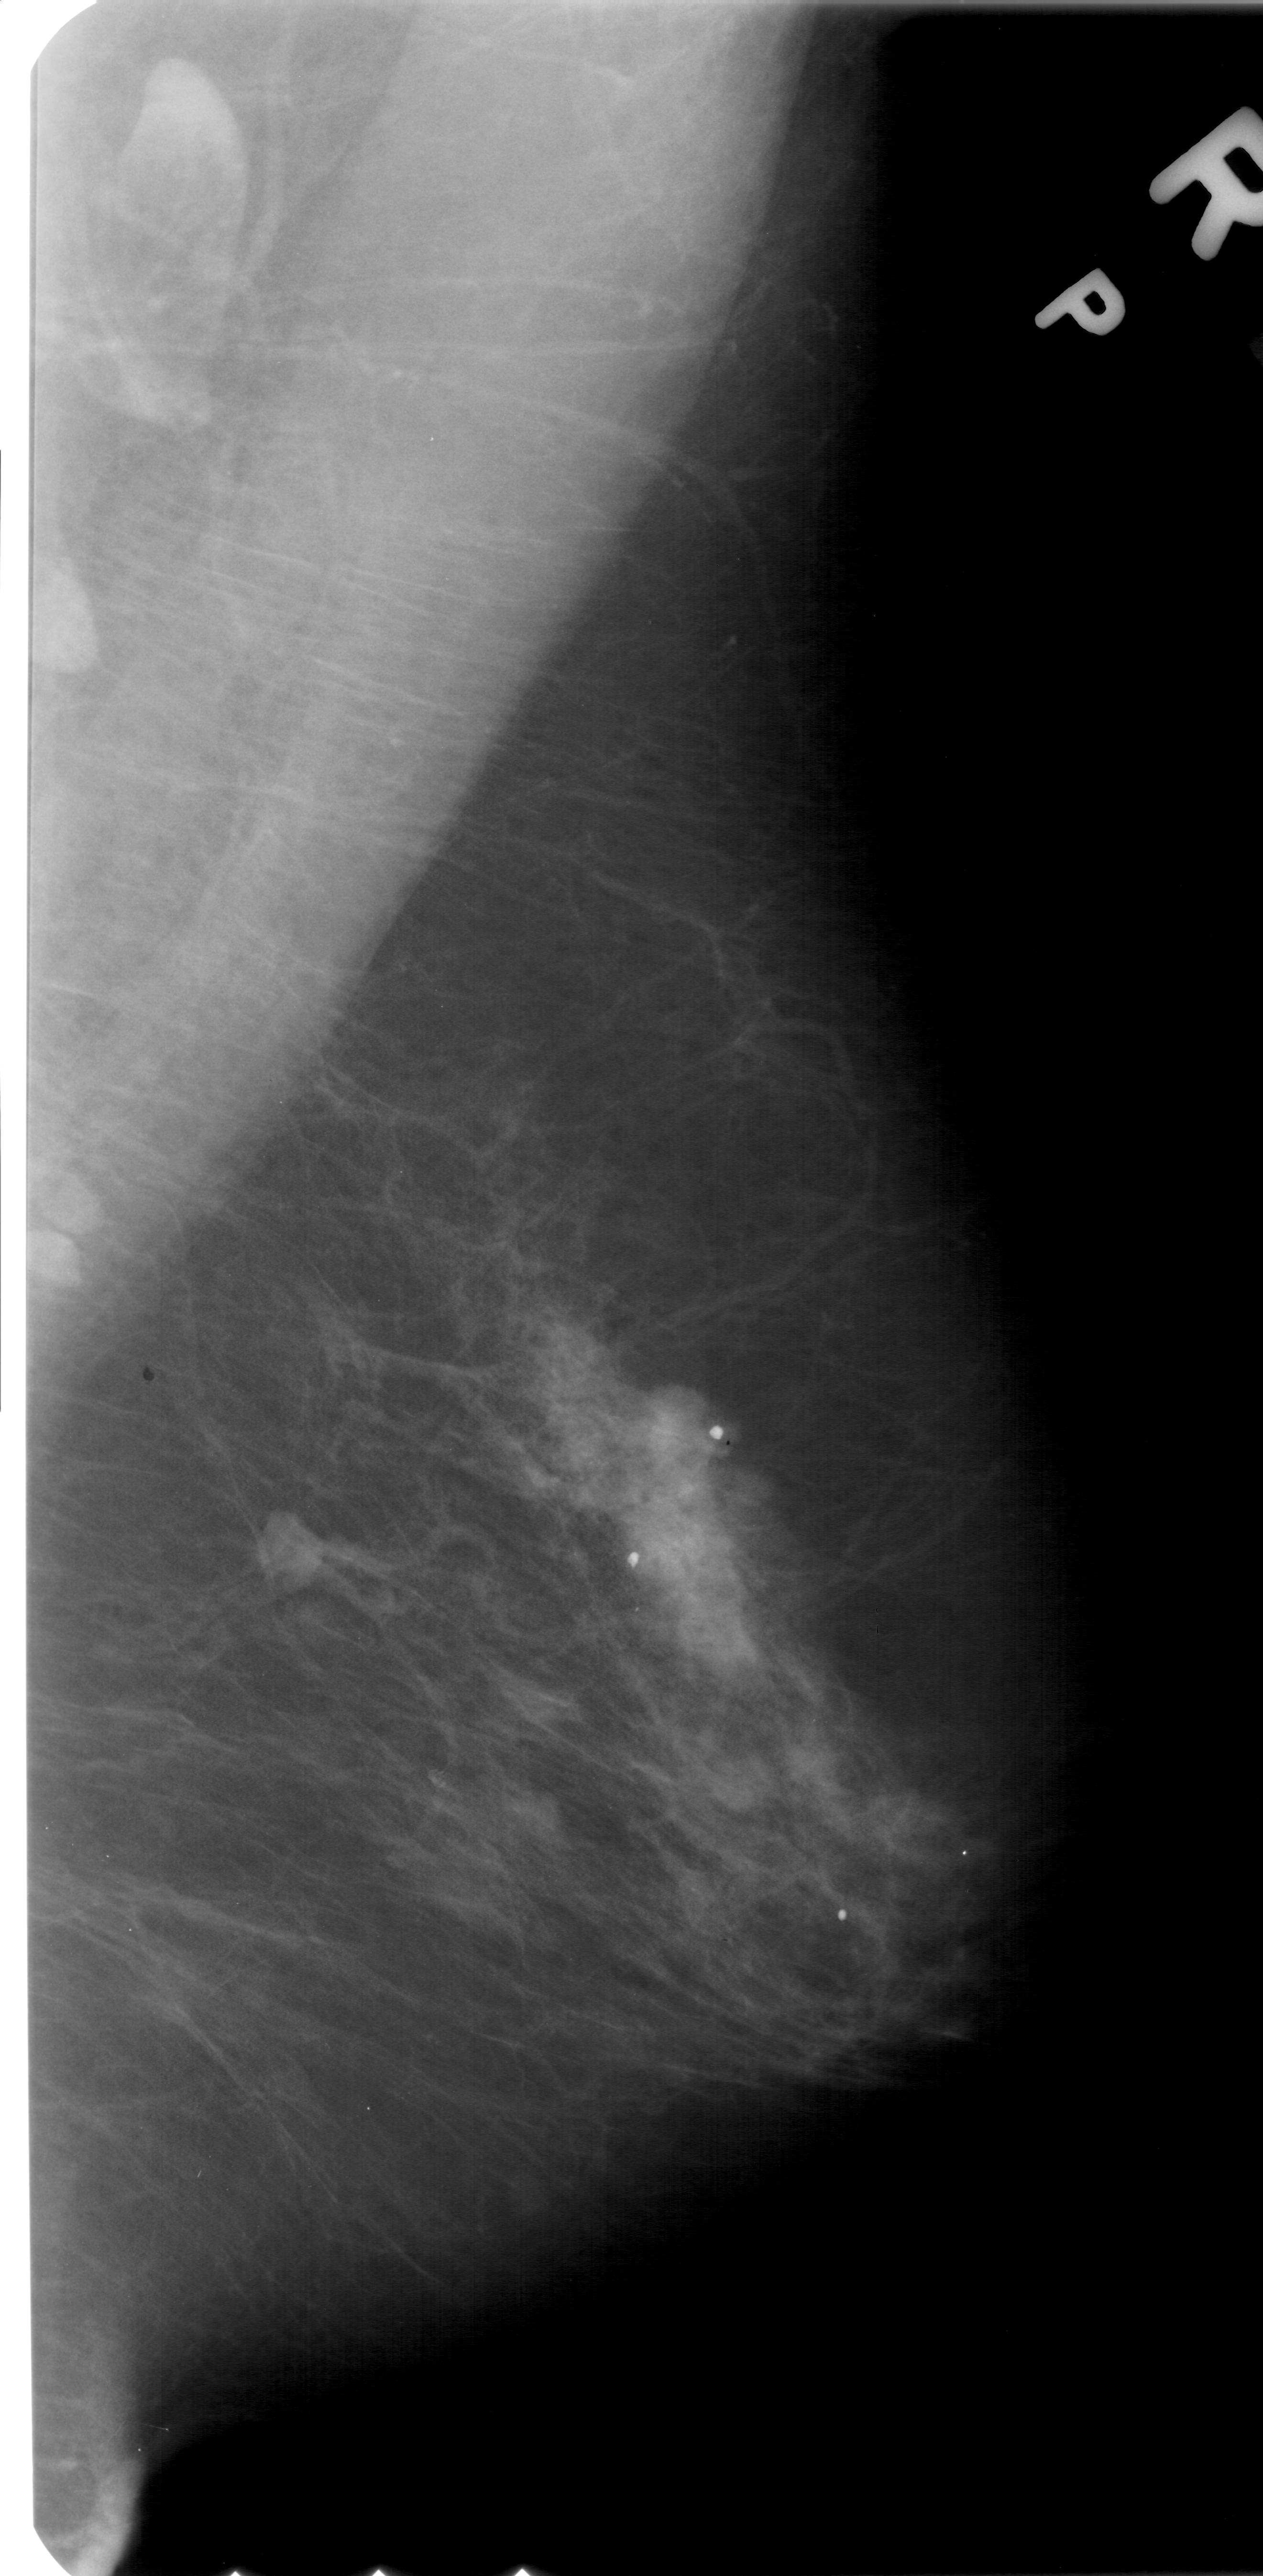
Mammogram (digitized film). Right breast. Mediolateral oblique (MLO) view. BI-RADS breast density category 3 (scale 1–4). 1263 × 2576 image matrix.
Expert-marked regions of interest on this film, with their recorded descriptors:
- mass, shape lobulated, margins circumscribed; BI-RADS assessment category 4; pathology (as recorded): benign: bounding box [x1, y1, x2, y2] px = [212, 1500, 355, 1602]